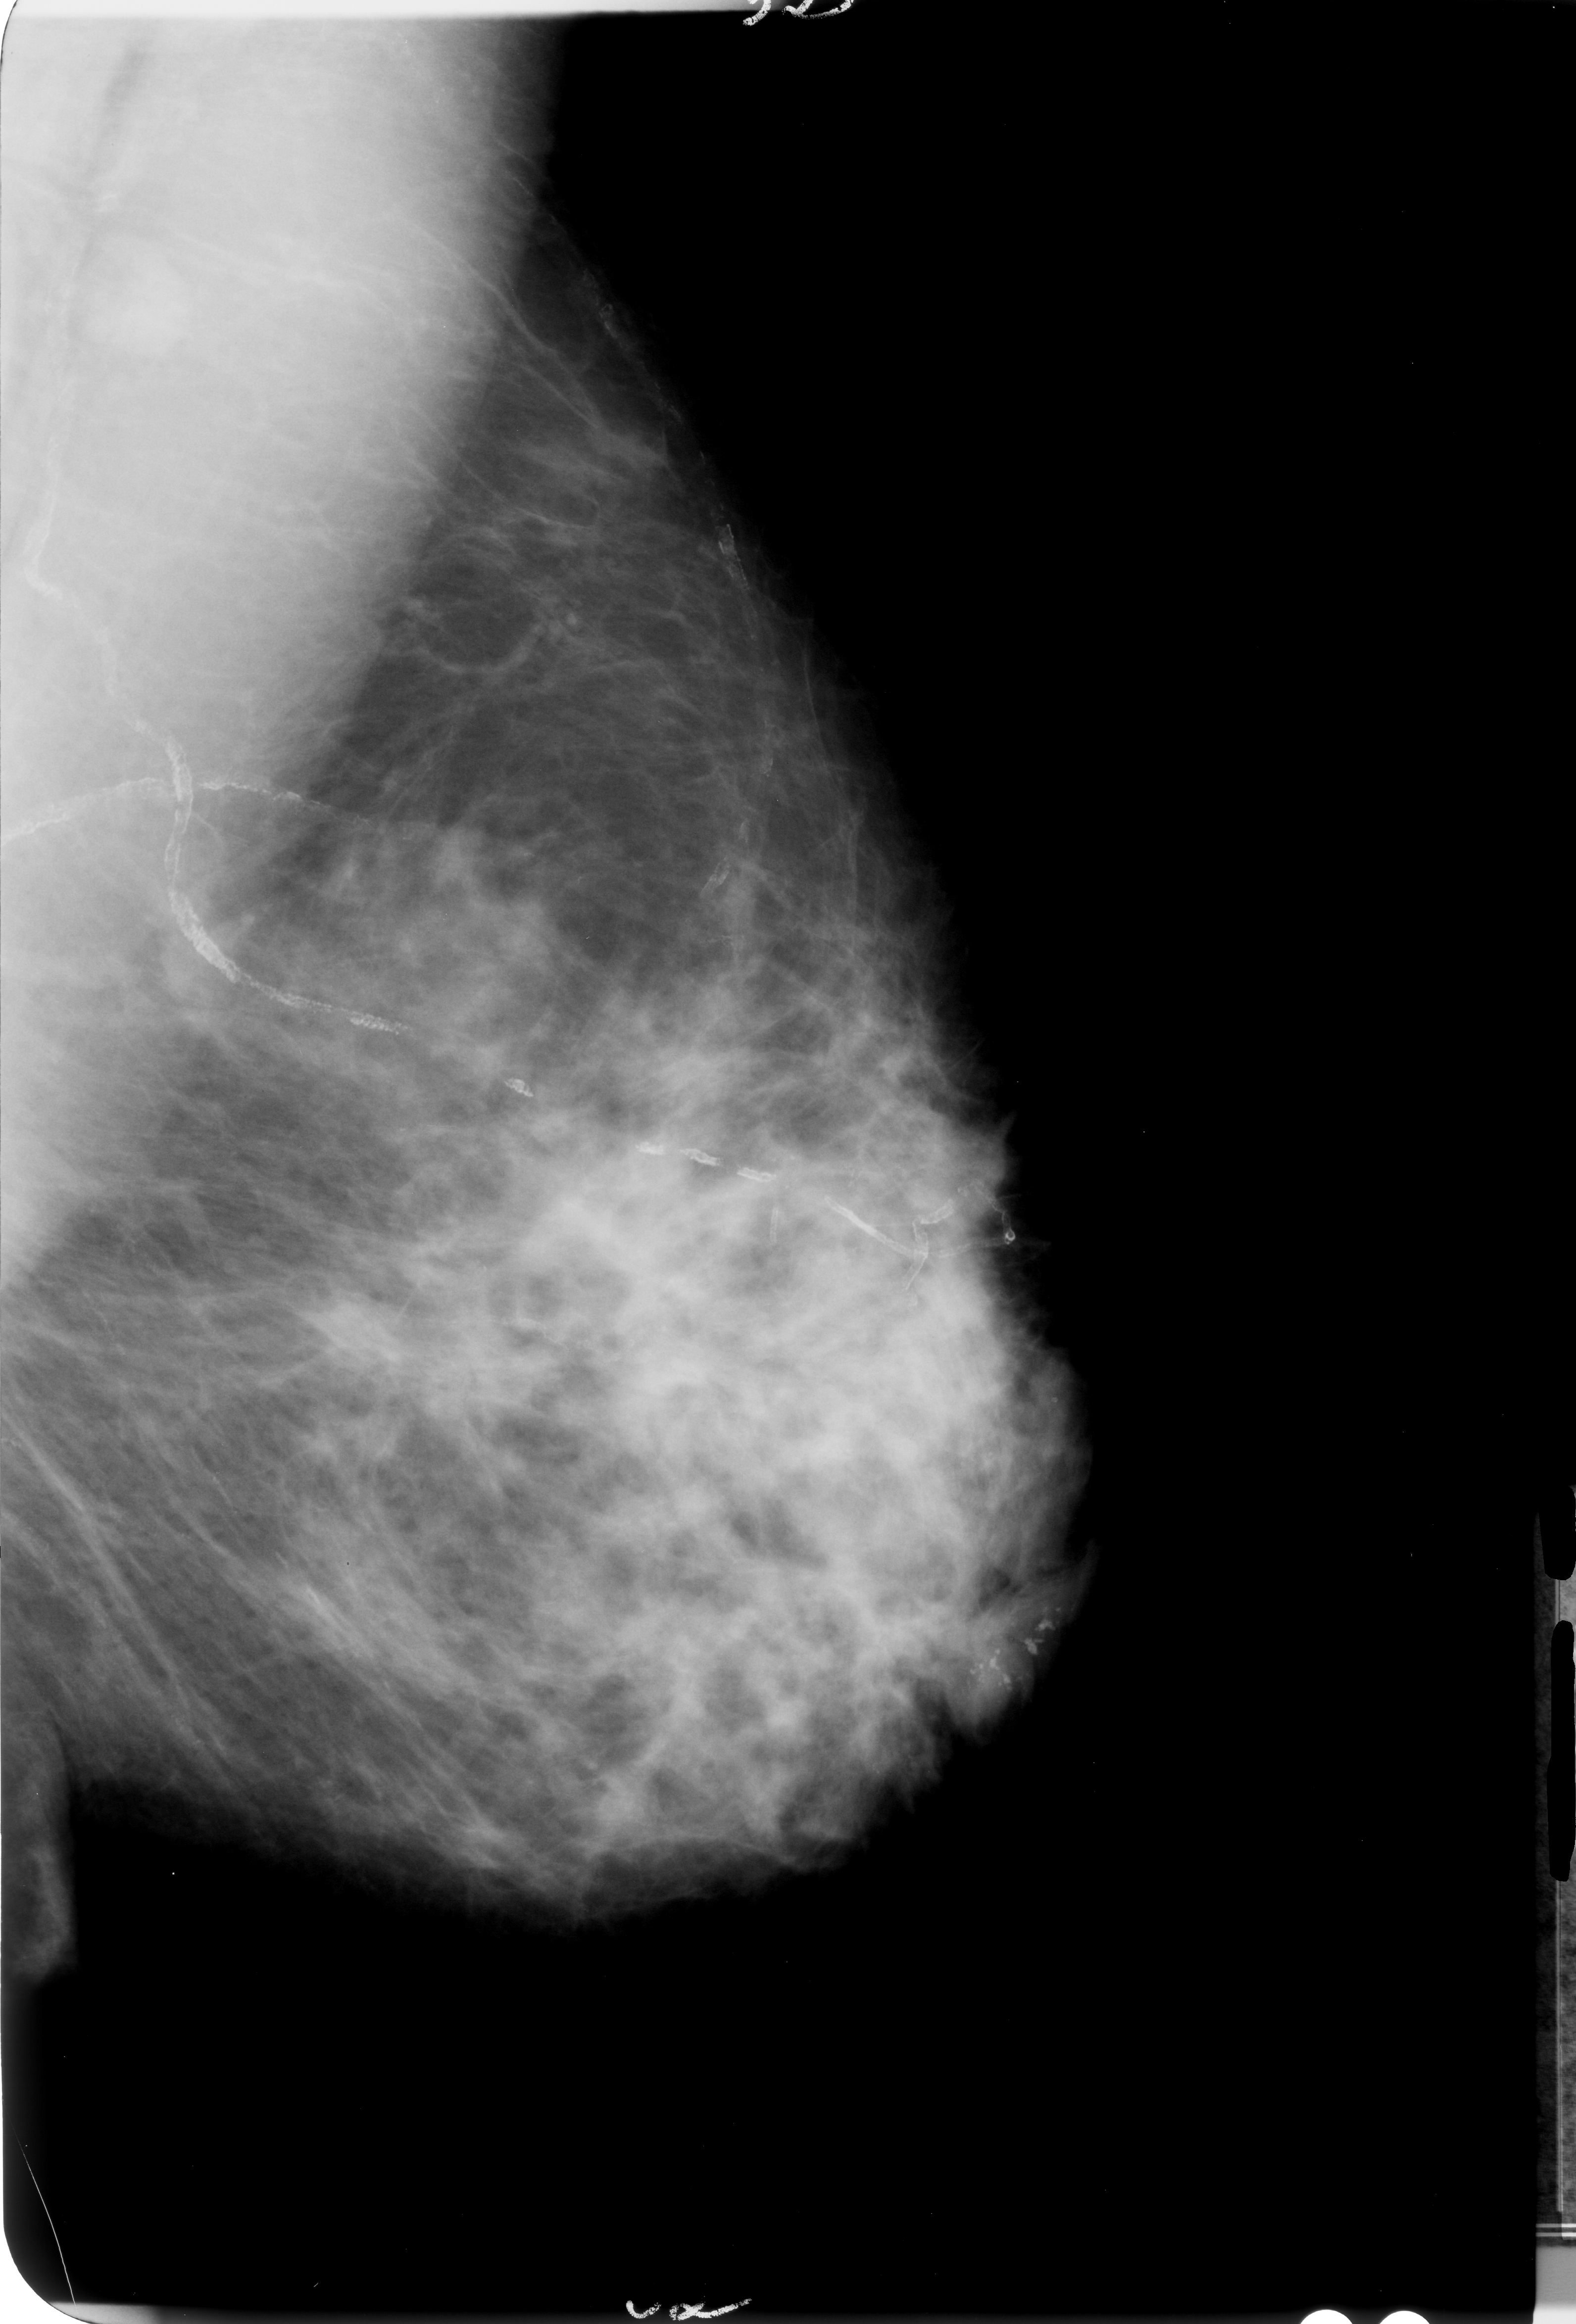
Mammogram (digitized film); left breast; MLO view; breast composition: scattered fibroglandular densities (BI-RADS density category 2 of 4); 1576 × 2324 image matrix.
Expert-marked regions of interest on this image (one box per marked abnormality):
- calcifications, morphology pleomorphic, distribution clustered; BI-RADS assessment category 4; pathology result (as recorded, not read from the image): malignant: bounding box (x1, y1, x2, y2) in pixels: (942, 1551, 1118, 1751)